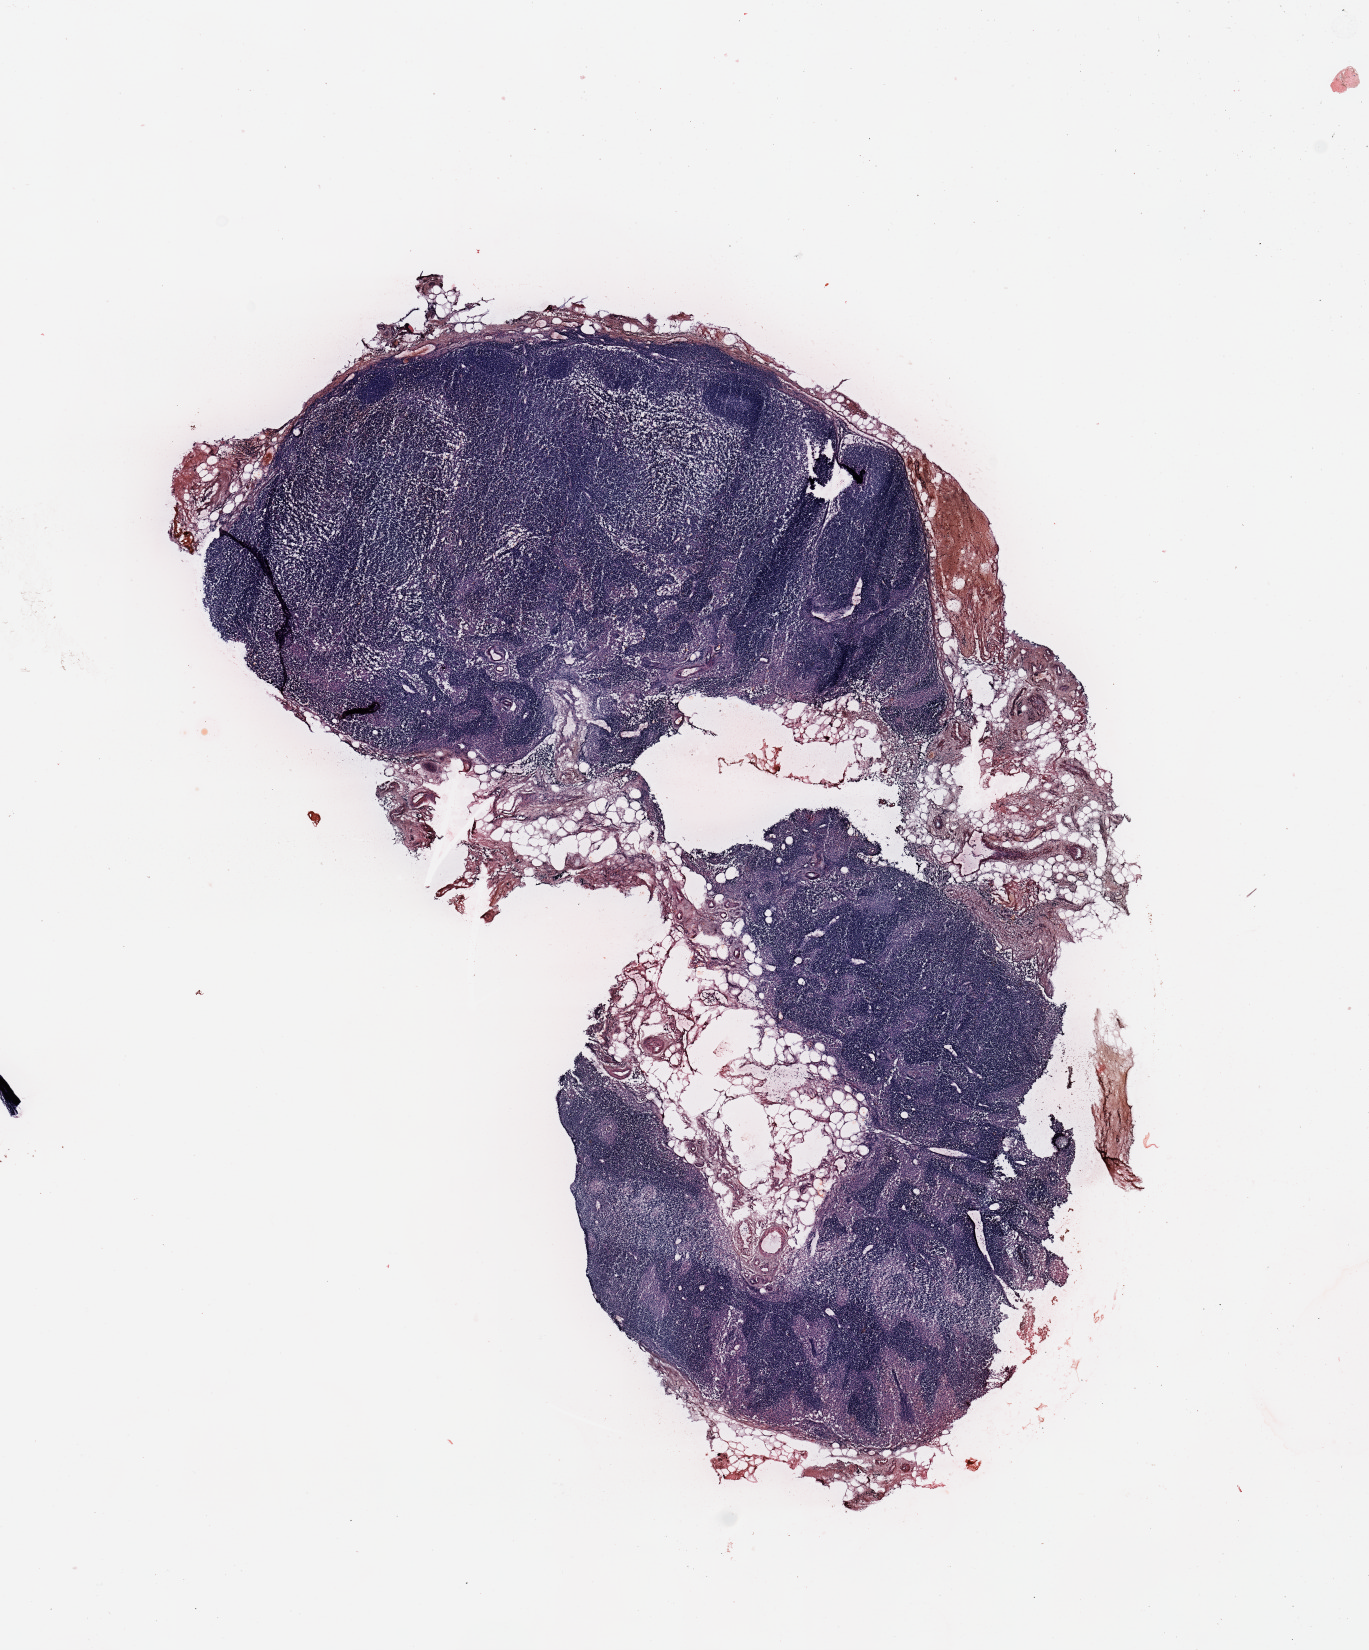
Digitized H&E tissue section (whole slide), a low-resolution overview of the entire scanned area, about 10.8 x 13.1 mm (acquisition: 20x scan), melanoma tumour tissue; sampled site not recorded. Patient: male, age 66 years.
Patient diagnosis (cohort enrolment): cutaneous melanoma (skin).